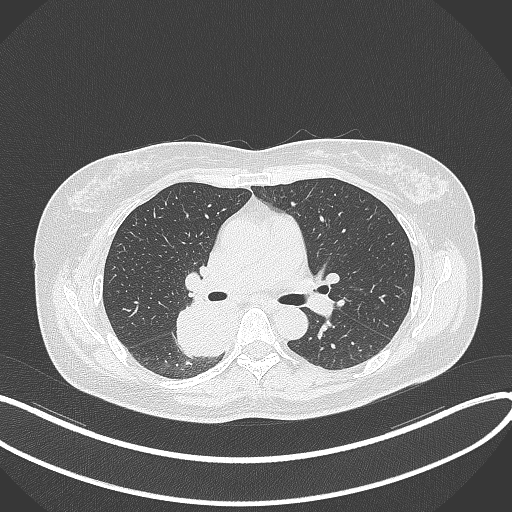
Chest CT, one axial slice. Position 215 of 331 along the scan axis. 120 kVp. Lung window (W 1500 / L -600 HU). 512 × 512 image matrix. Patient: female, 54 years. From the clinical record (not read from this slice): clinical TNM (as recorded): T4 N0 M0.
Structures marked on this image (bounding box drawn by a radiologist):
- lung tumour (recorded histology: adenocarcinoma): bounding box (x1, y1, x2, y2) in pixels: (171, 300, 233, 360)